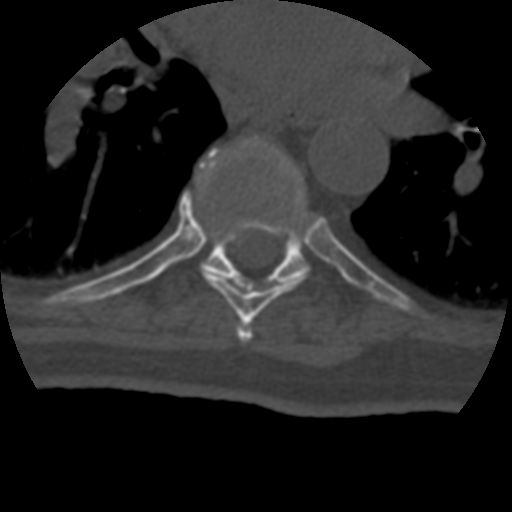
CT including the spine, one axial slice; slice 272 of 399 in the series (ordered by position); 120 kVp; bone window (W 1800 / L 400 HU); 1.25 mm slice thickness; 512 × 512 image matrix, field of view 160 × 160 mm. Patient age 69 years. From the clinical record (not read from this slice): primary cancer: prostate.
Annotated regions visible in this slice (semi-automatically segmented with operator editing):
- T6 vertebra: bounding box (x1, y1, x2, y2) in pixels: (237, 325, 252, 342)
- T7 vertebra: (198, 137, 296, 324)
- T8 vertebra: (202, 138, 310, 283)